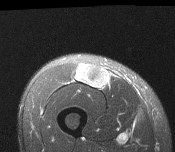
MRI of an extremity soft-tissue mass, one axial slice; slice 49 of 116 in the series (ordered by position); T2-weighted fat-saturated; MR volume resampled by the dataset authors to the PET/CT grid (not the native acquisition matrix); 175 × 152 image matrix, field of view 171 × 148 mm. Male patient. Case-level facts recorded for this patient, not image findings: histological type: pleiomorphic leiomyosarcoma; grade: intermediate; site of the primary tumour: right thigh.
Structures marked on this image (expert contour drawn on MRI and transferred to this co-registered scan by the dataset authors):
- gross tumour volume including surrounding oedema: bounding box (x1, y1, x2, y2) in pixels: (76, 65, 109, 89)